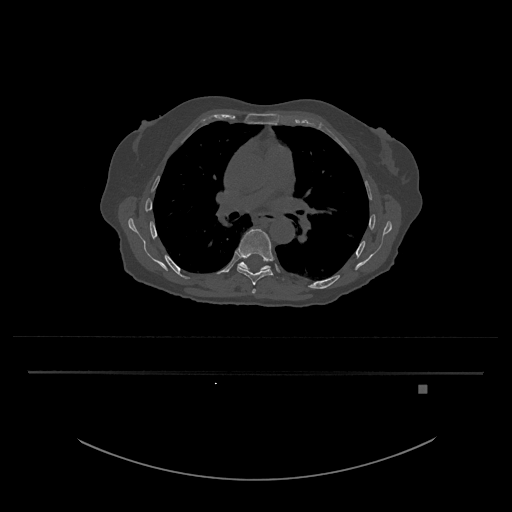
CT including the spine, one axial slice. Position 795 of 797 along the scan axis. Reconstruction kernel Br40s/3. 120 kVp. Bone window (W 1800 / L 400 HU). 0.5 mm slice thickness. 512 × 512 image matrix, field of view 500 × 500 mm. Patient: female, 57 years. From the clinical record (not read from this slice): primary cancer: cervical.
Structures marked on this image (semi-automatically segmented with operator editing):
- T8 vertebra: bounding box <236,229,284,285> (left, top, right, bottom; pixels)
- T9 vertebra: <238,259,271,272>